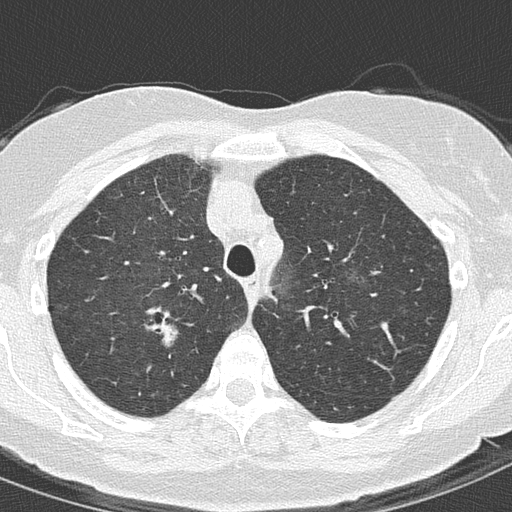
Low-dose screening chest CT, axial slice, second annual screen, lung window (W 1500 / L -600 HU), 120 kVp, 512 × 512 image matrix. Female, age 61 years at enrolment. Current smoker at enrolment.
- Expert-annotated lung lesion, box from (x=146, y=306) to (x=188, y=344) px.
- The exam's reader record, not a measurement of the box and not confirmed to be the same lesion: non-calcified nodule or mass ≥4 mm, right upper lobe, 15 × 10 mm, spiculated (stellate) margins, ground glass attenuation, pre-existing on the prior screen: yes; interval growth: yes.
- Official screen result: positive, other.
- Later outcome: lung cancer diagnosed 91 days after this screen — adenocarcinoma, NOS, right upper lobe, moderately differentiated (G2), stage IA (AJCC 6th edition), 20 mm at pathology.